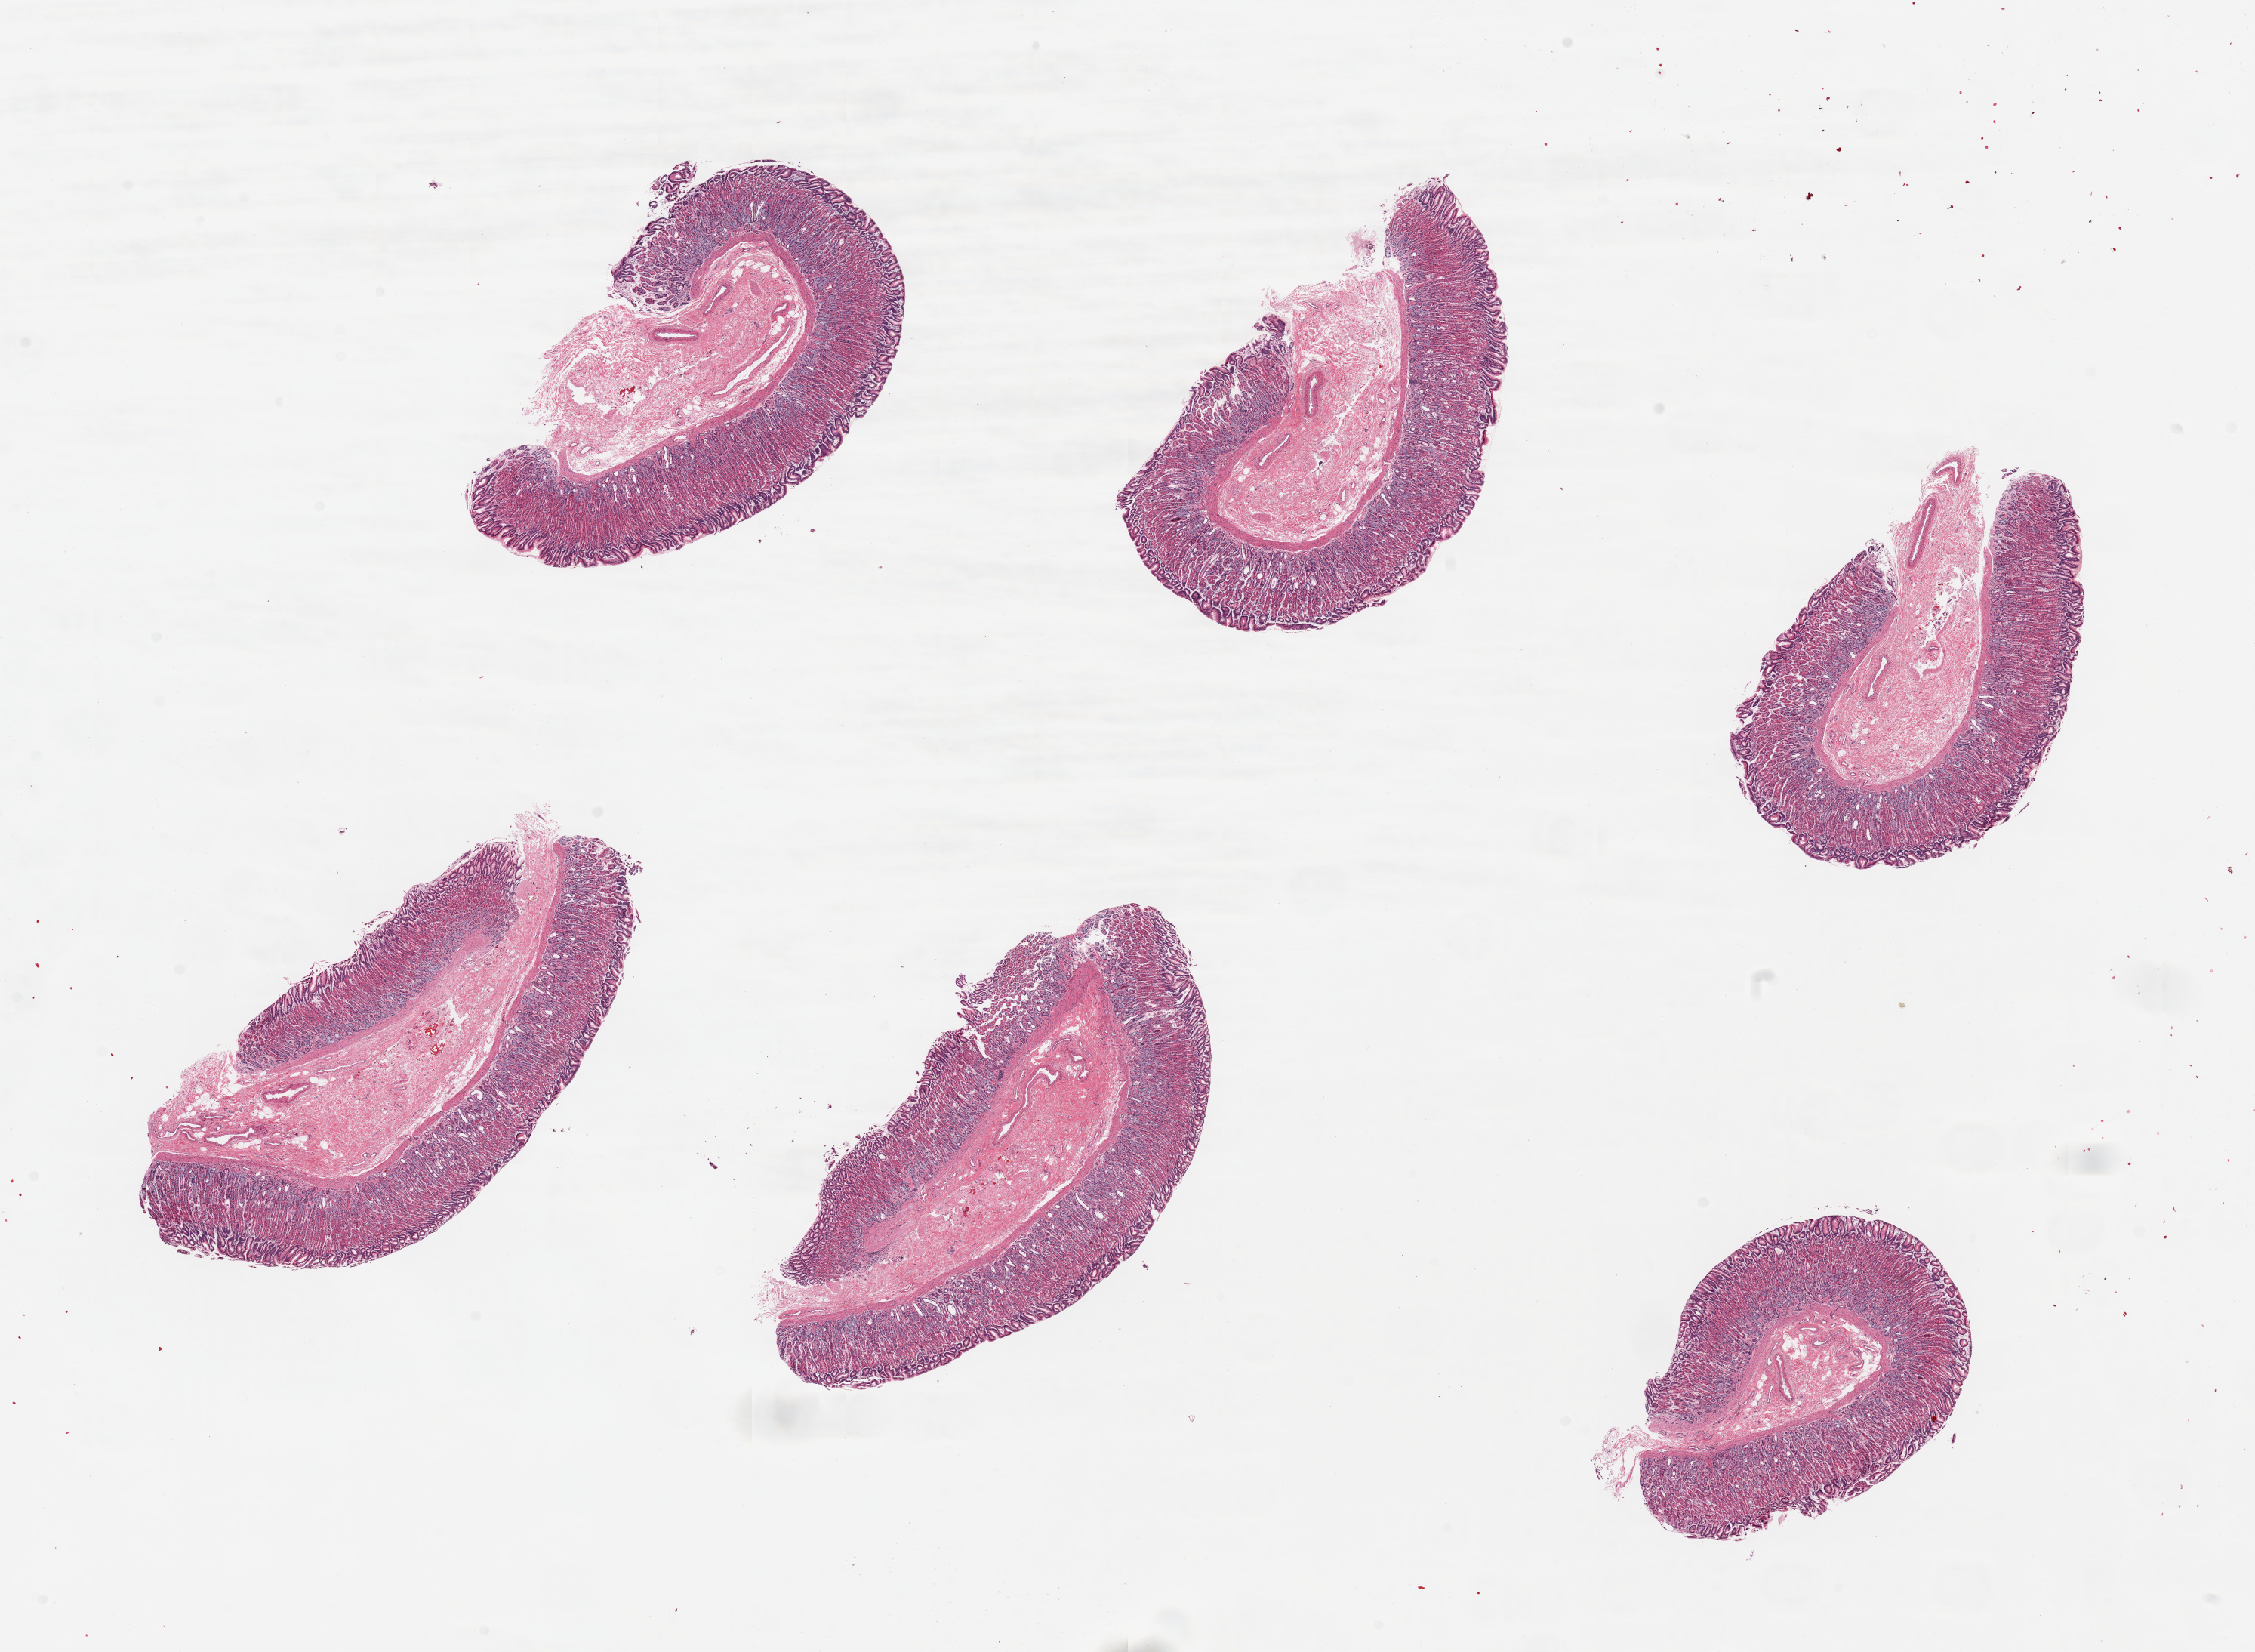
Haematoxylin and eosin whole-slide image, whole scanned area (about 23.6 x 17.3 mm, from a 20x scan) shown as a low-resolution overview; PAXgene-fixed paraffin-embedded (PFPE) section; target tissue: stomach; donor tissue sample. Female donor.
* pathologist's review note for this sample: 6 pieces, exceptionally well-preserved mucosa, up to ~1mm, ~30-40% thickness